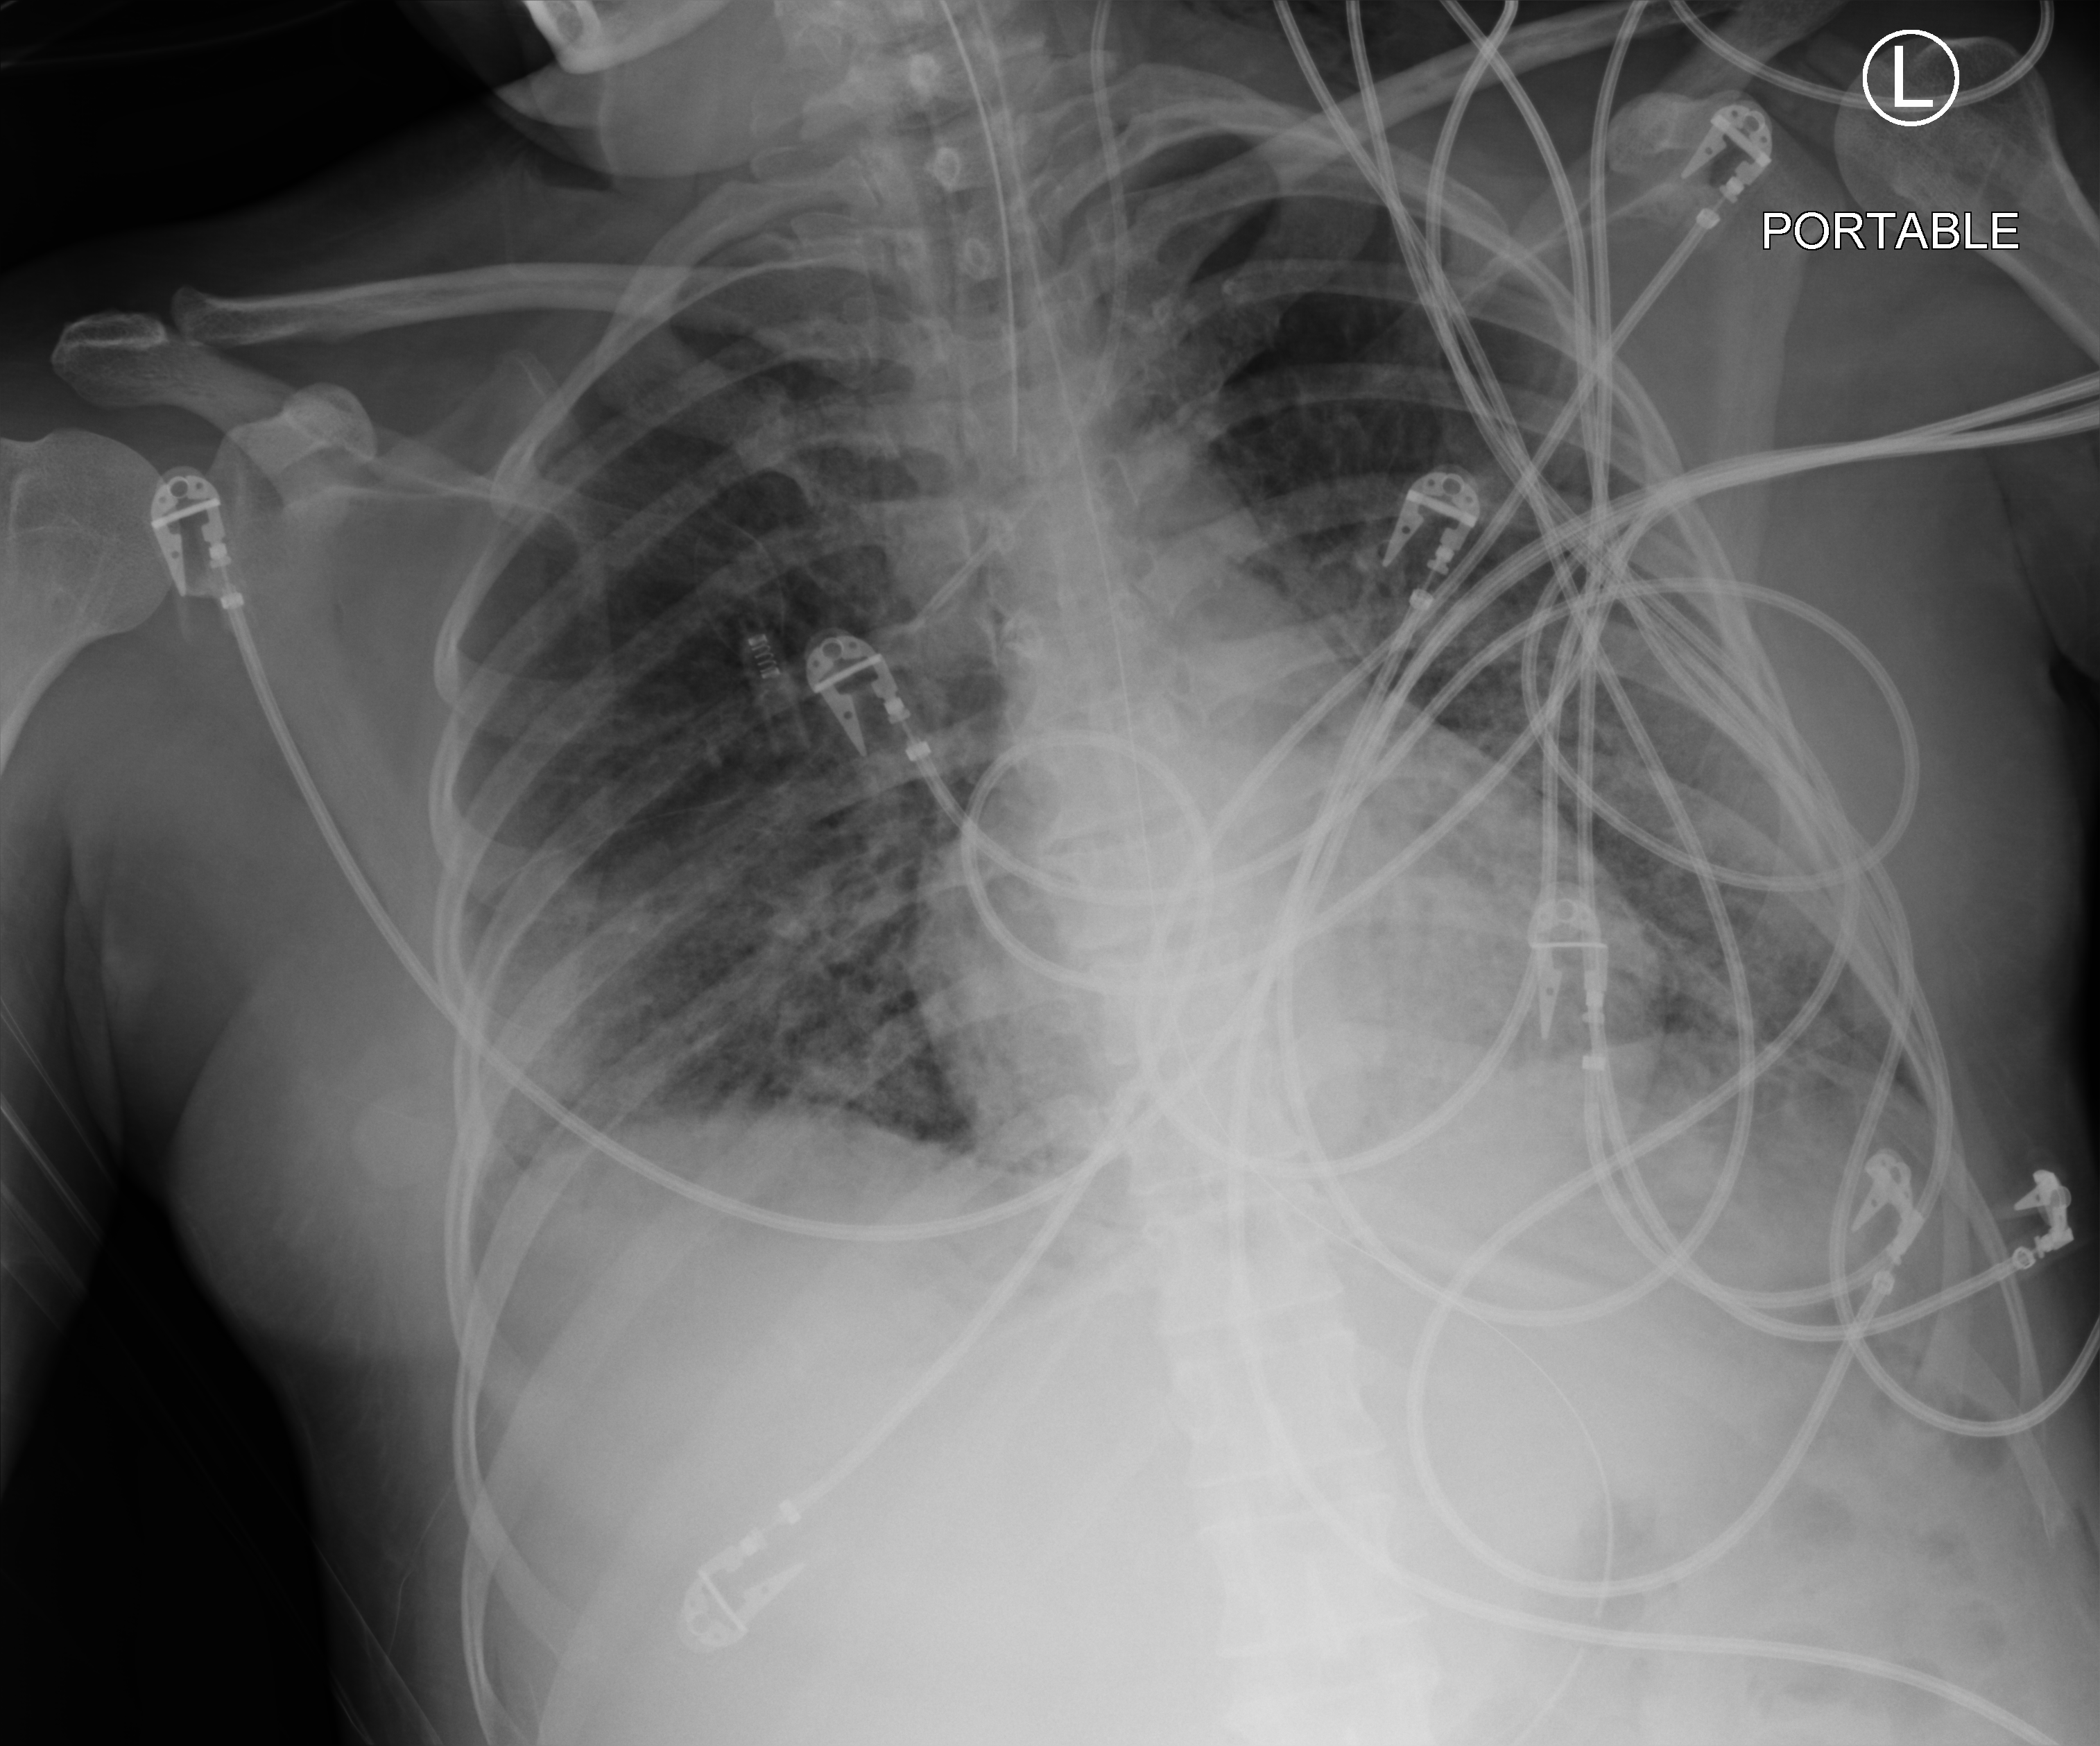
Portable chest radiograph; anteroposterior (AP) projection. Patient hospitalised with COVID-19; female, aged 18–59 years.
Admission-level facts for this patient (not findings on this image; timing relative to this image not recorded): hypertension (admission record): no; admitted to intensive care during this hospital stay: yes; mechanically ventilated during this hospital stay: yes.